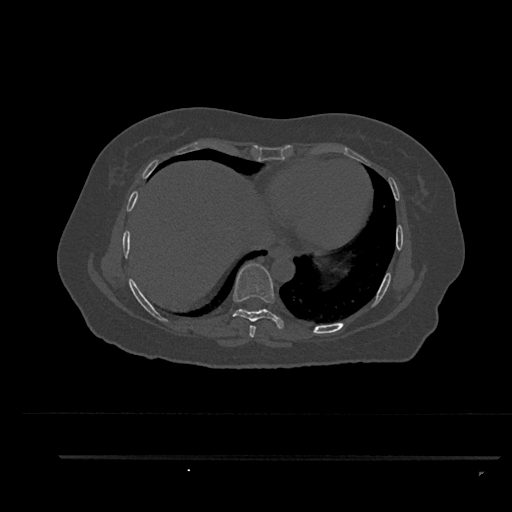
CT including the spine, one axial slice; position 459 of 797 along the scan axis; 120 kVp; bone window (W 1800 / L 400 HU); 512 × 512 image matrix, field of view 408 × 408 mm. Patient: female, 44 years. From the clinical record (not read from this slice): primary cancer: renal.
Outlined on this slice (semi-automatically segmented with operator editing):
- T7 vertebra: bounding box [x1, y1, x2, y2] px = [249, 325, 256, 338]
- T8 vertebra: [232, 263, 285, 329]